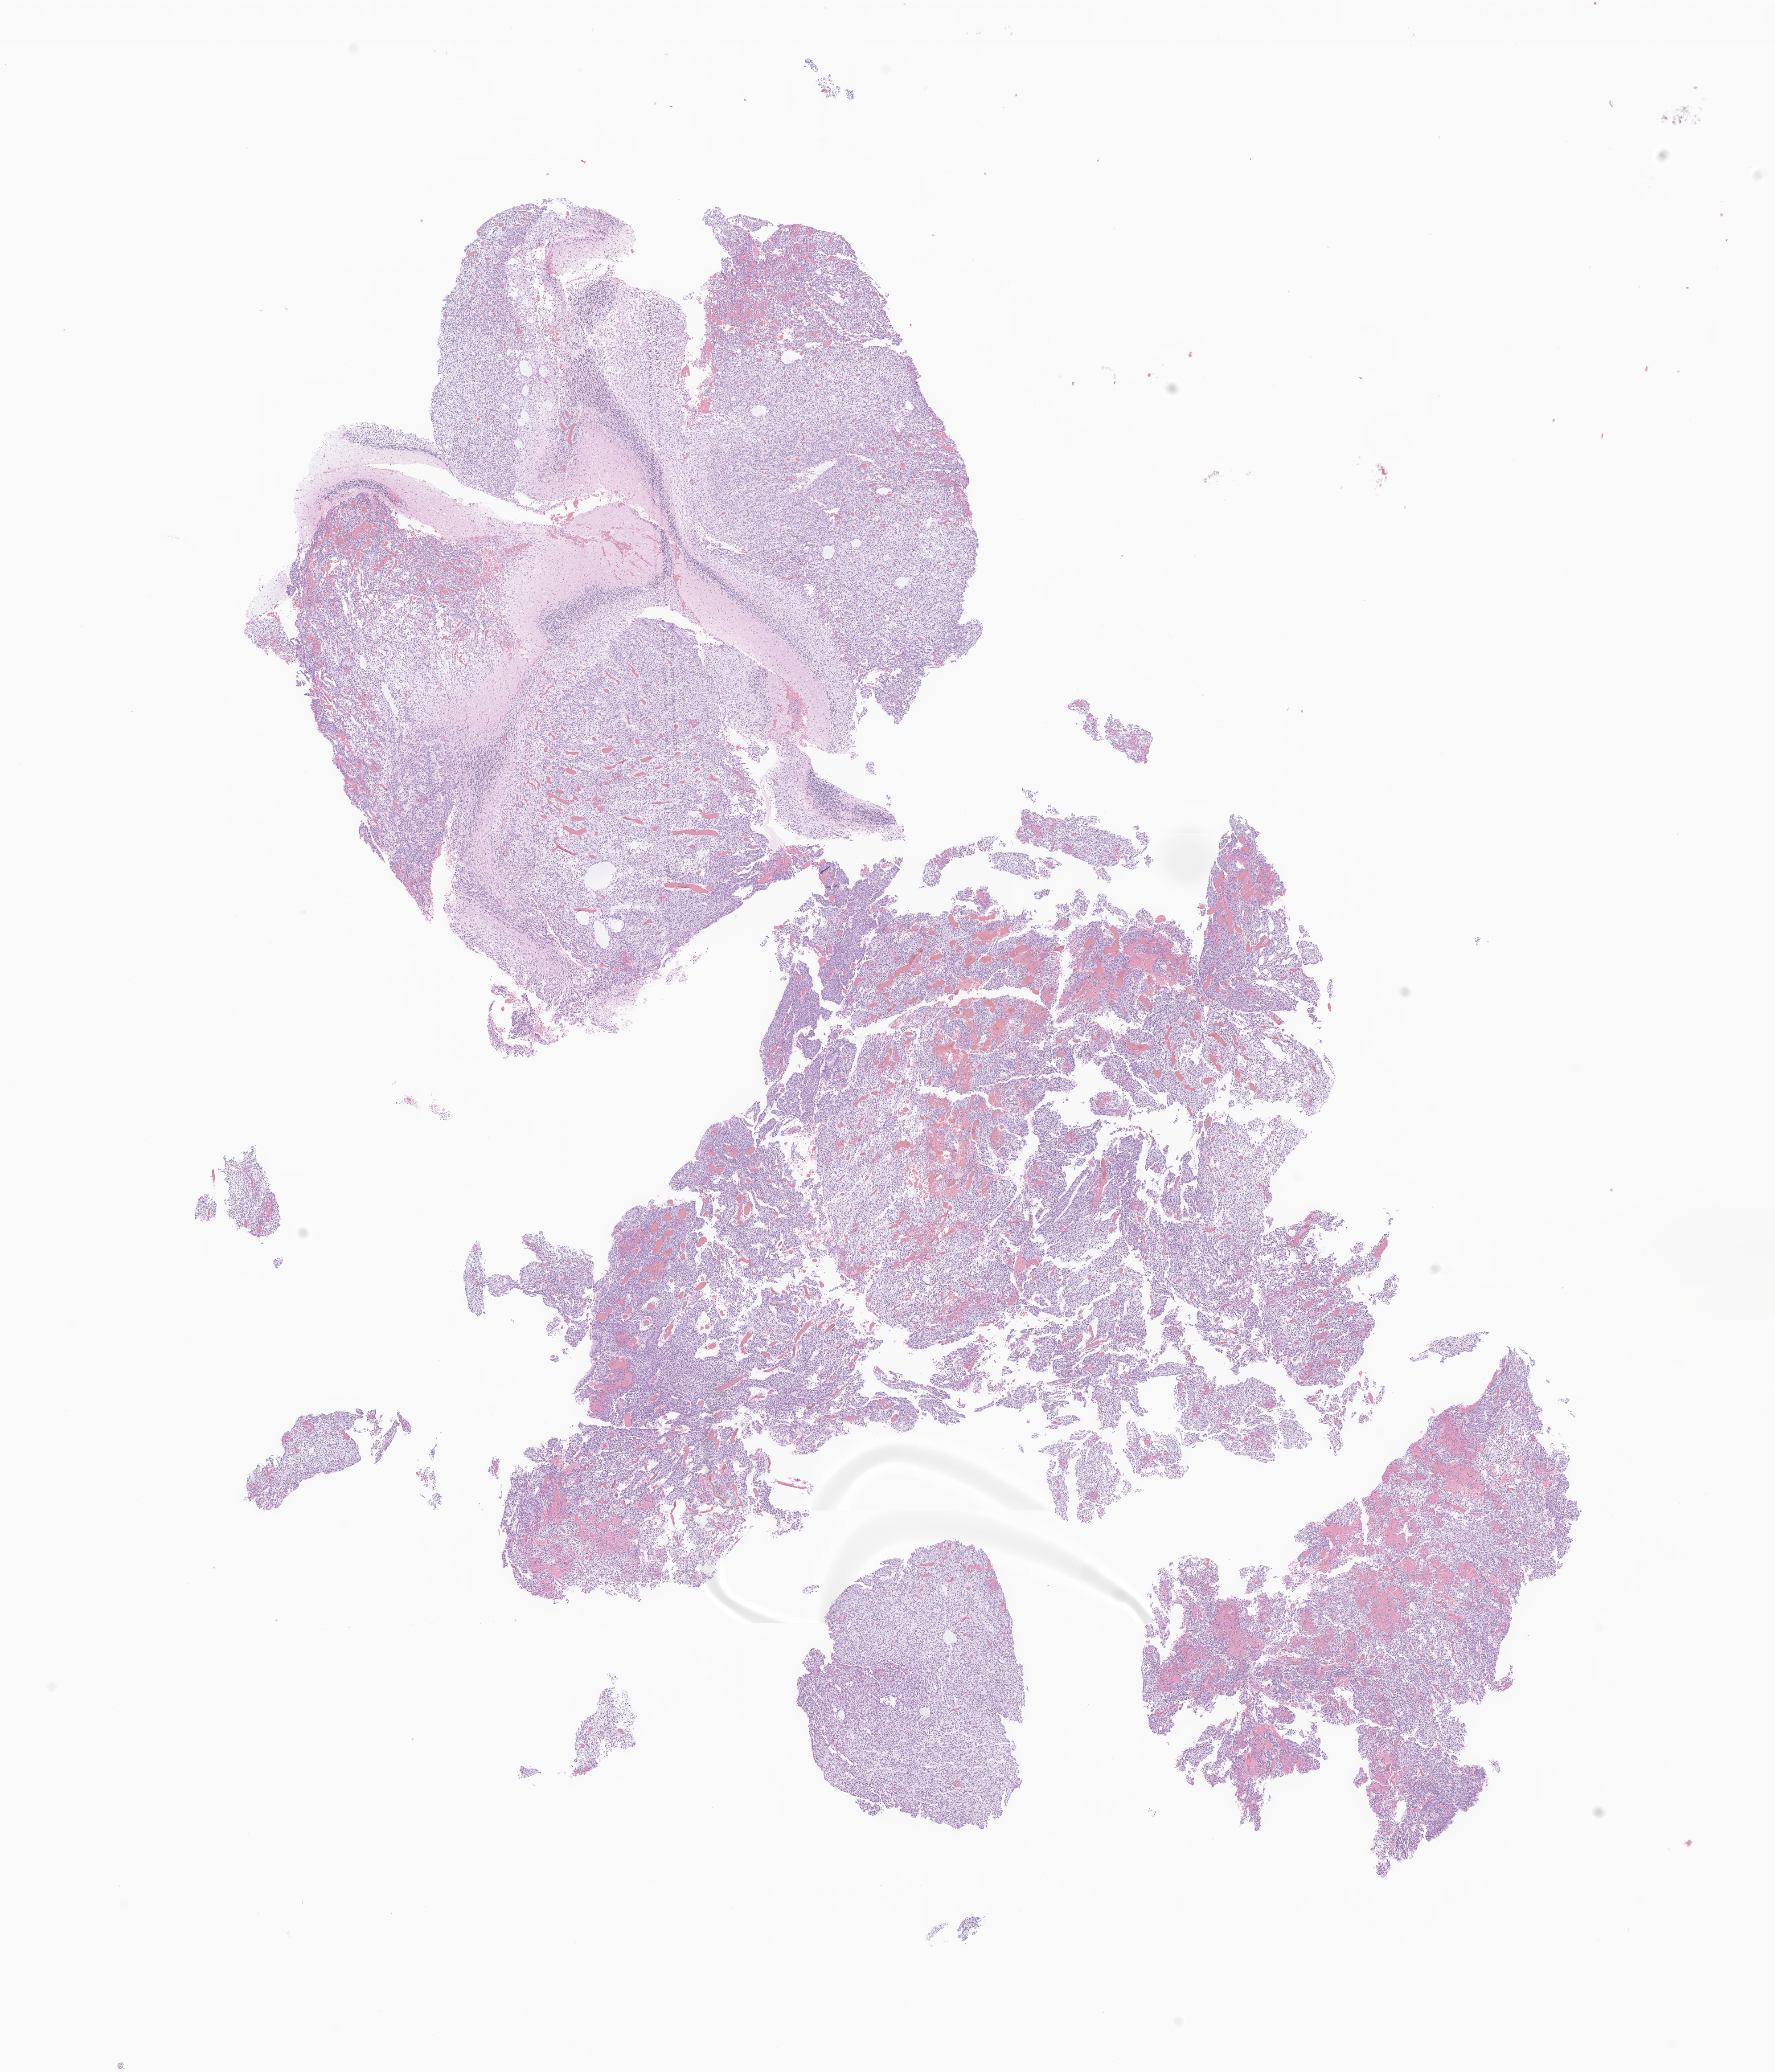
H&E whole-slide image of tumor tissue from the cerebral ventricle — low-resolution overview of the scanned area, about 16.8 x 19.6 mm, FFPE section. Patient female; age 755 days.
Diagnosis: Neoplasm, malignant.